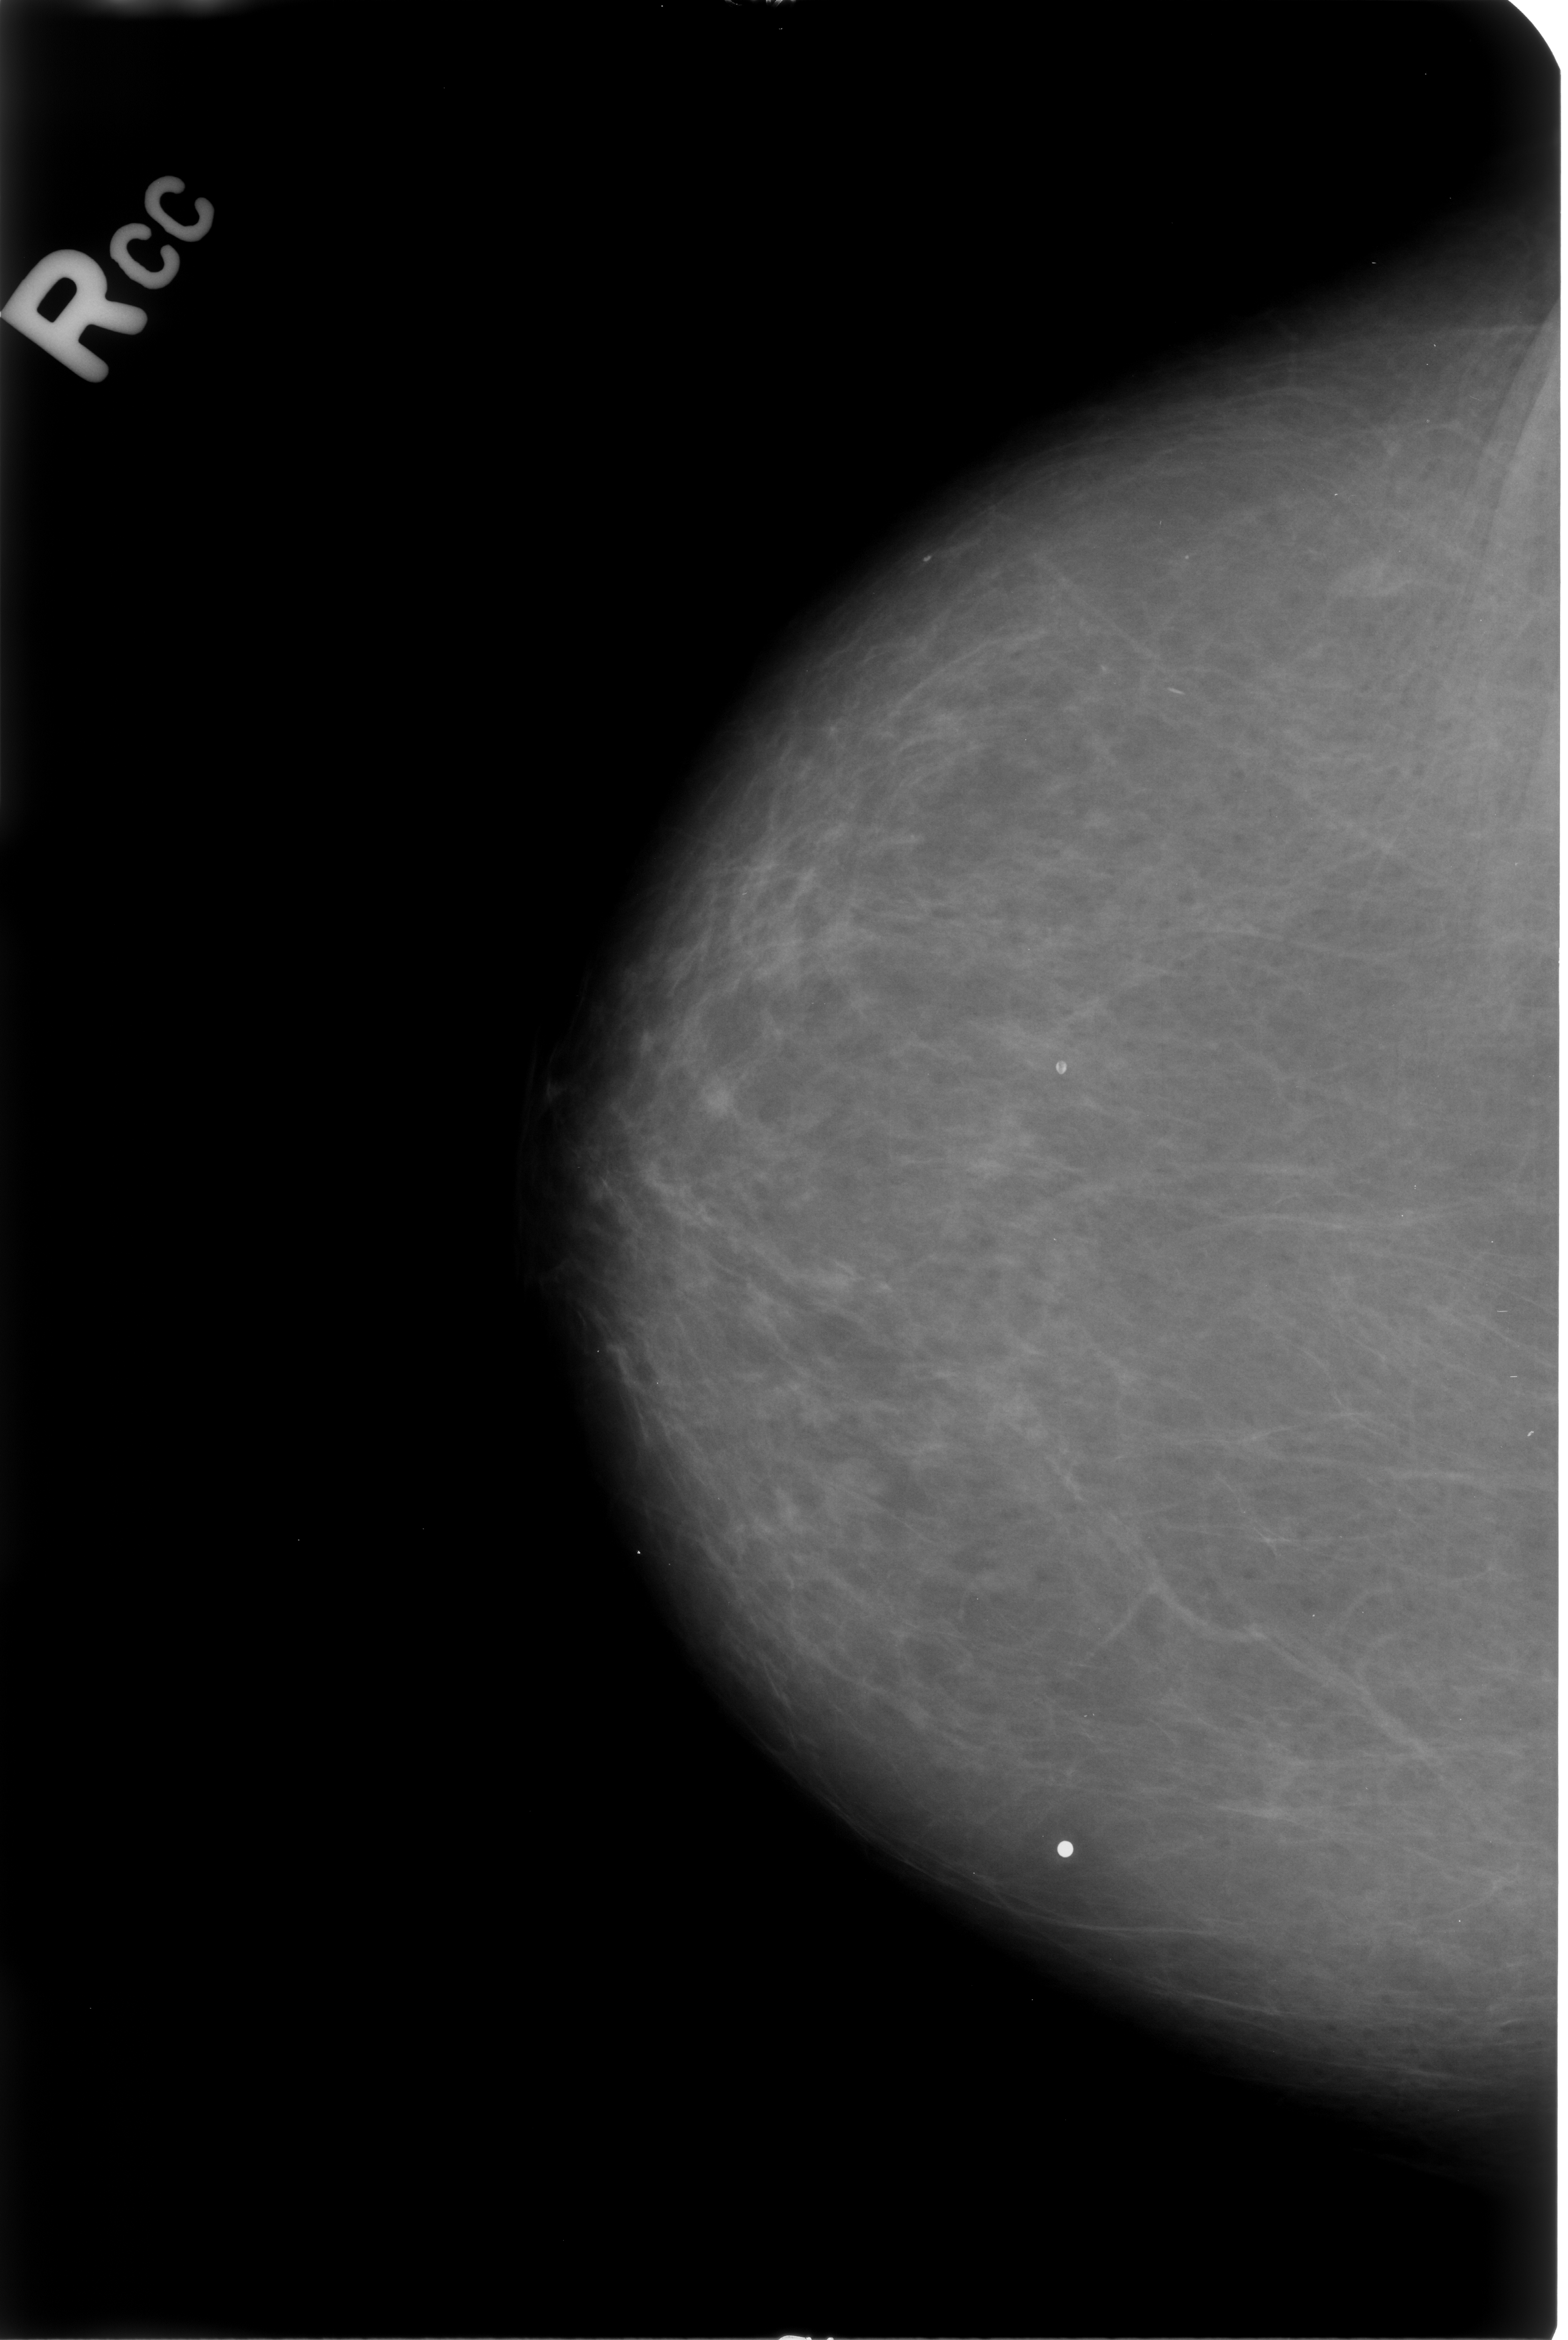
Mammogram (digitized film). Right breast. CC view. Breast composition: almost entirely fatty (BI-RADS density category 1 of 4). 1568 × 2340 image matrix.
Expert-marked regions of interest on this film, with their recorded descriptors:
- Finding 1 of 2: calcifications, morphology lucent center; BI-RADS assessment category 2; outcome (as recorded, no biopsy): benign without callback (not worked up further): box from (x=909, y=528) to (x=984, y=566) px
- Finding 2 of 2: calcifications, morphology lucent center; BI-RADS assessment category 2; outcome (as recorded, no biopsy): benign without callback (not worked up further): (x=1039, y=1056)–(x=1082, y=1086)